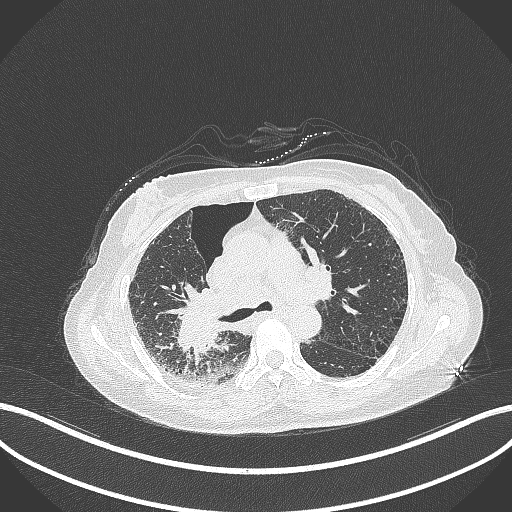
Chest CT, one axial slice; position 218 of 408 along the scan axis; lung window (W 1500 / L -600 HU); 1 mm slice thickness; 512 × 512 image matrix, field of view 400 × 400 mm. Female patient, age 64 years. Case-level facts recorded for this patient, not image findings: clinical TNM (as recorded): T3 N3 M0.
Annotated regions visible in this slice (rectangle marked by the reading radiologist):
- lung tumour (recorded histology: squamous cell carcinoma): bounding box <168,285,225,357> (left, top, right, bottom; pixels)